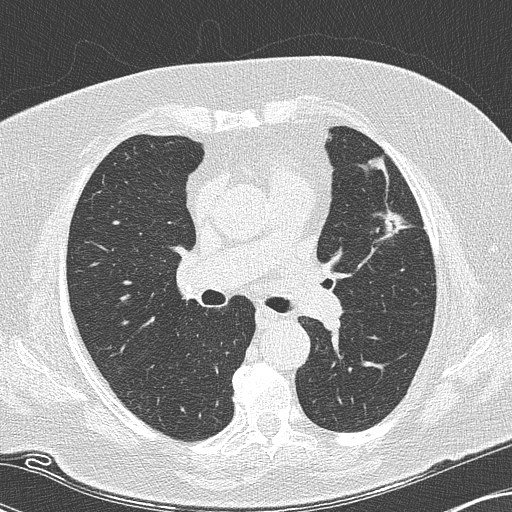
Chest CT (low-dose screening protocol), one axial image. Second screening round (one year after baseline). Lung window (W 1500 / L -600 HU). 2 mm slice thickness. Lung (sharp) reconstruction kernel (B50f). Slice 56 of 151 in the series. Female participant, aged 73 years at enrolment.
Lesion marked by an expert reader, box from (x=362, y=204) to (x=404, y=247) px. The screening reader recorded 2 non-calcified nodules or masses ≥4 mm on this exam; which of them this box marks is not recorded. Official screen result: positive, other. Later outcome: lung cancer diagnosed 123 days after this screen — adenocarcinoma, NOS, left upper lobe, moderately differentiated (G2), stage IIIB (AJCC 6th edition), 12 mm at pathology.